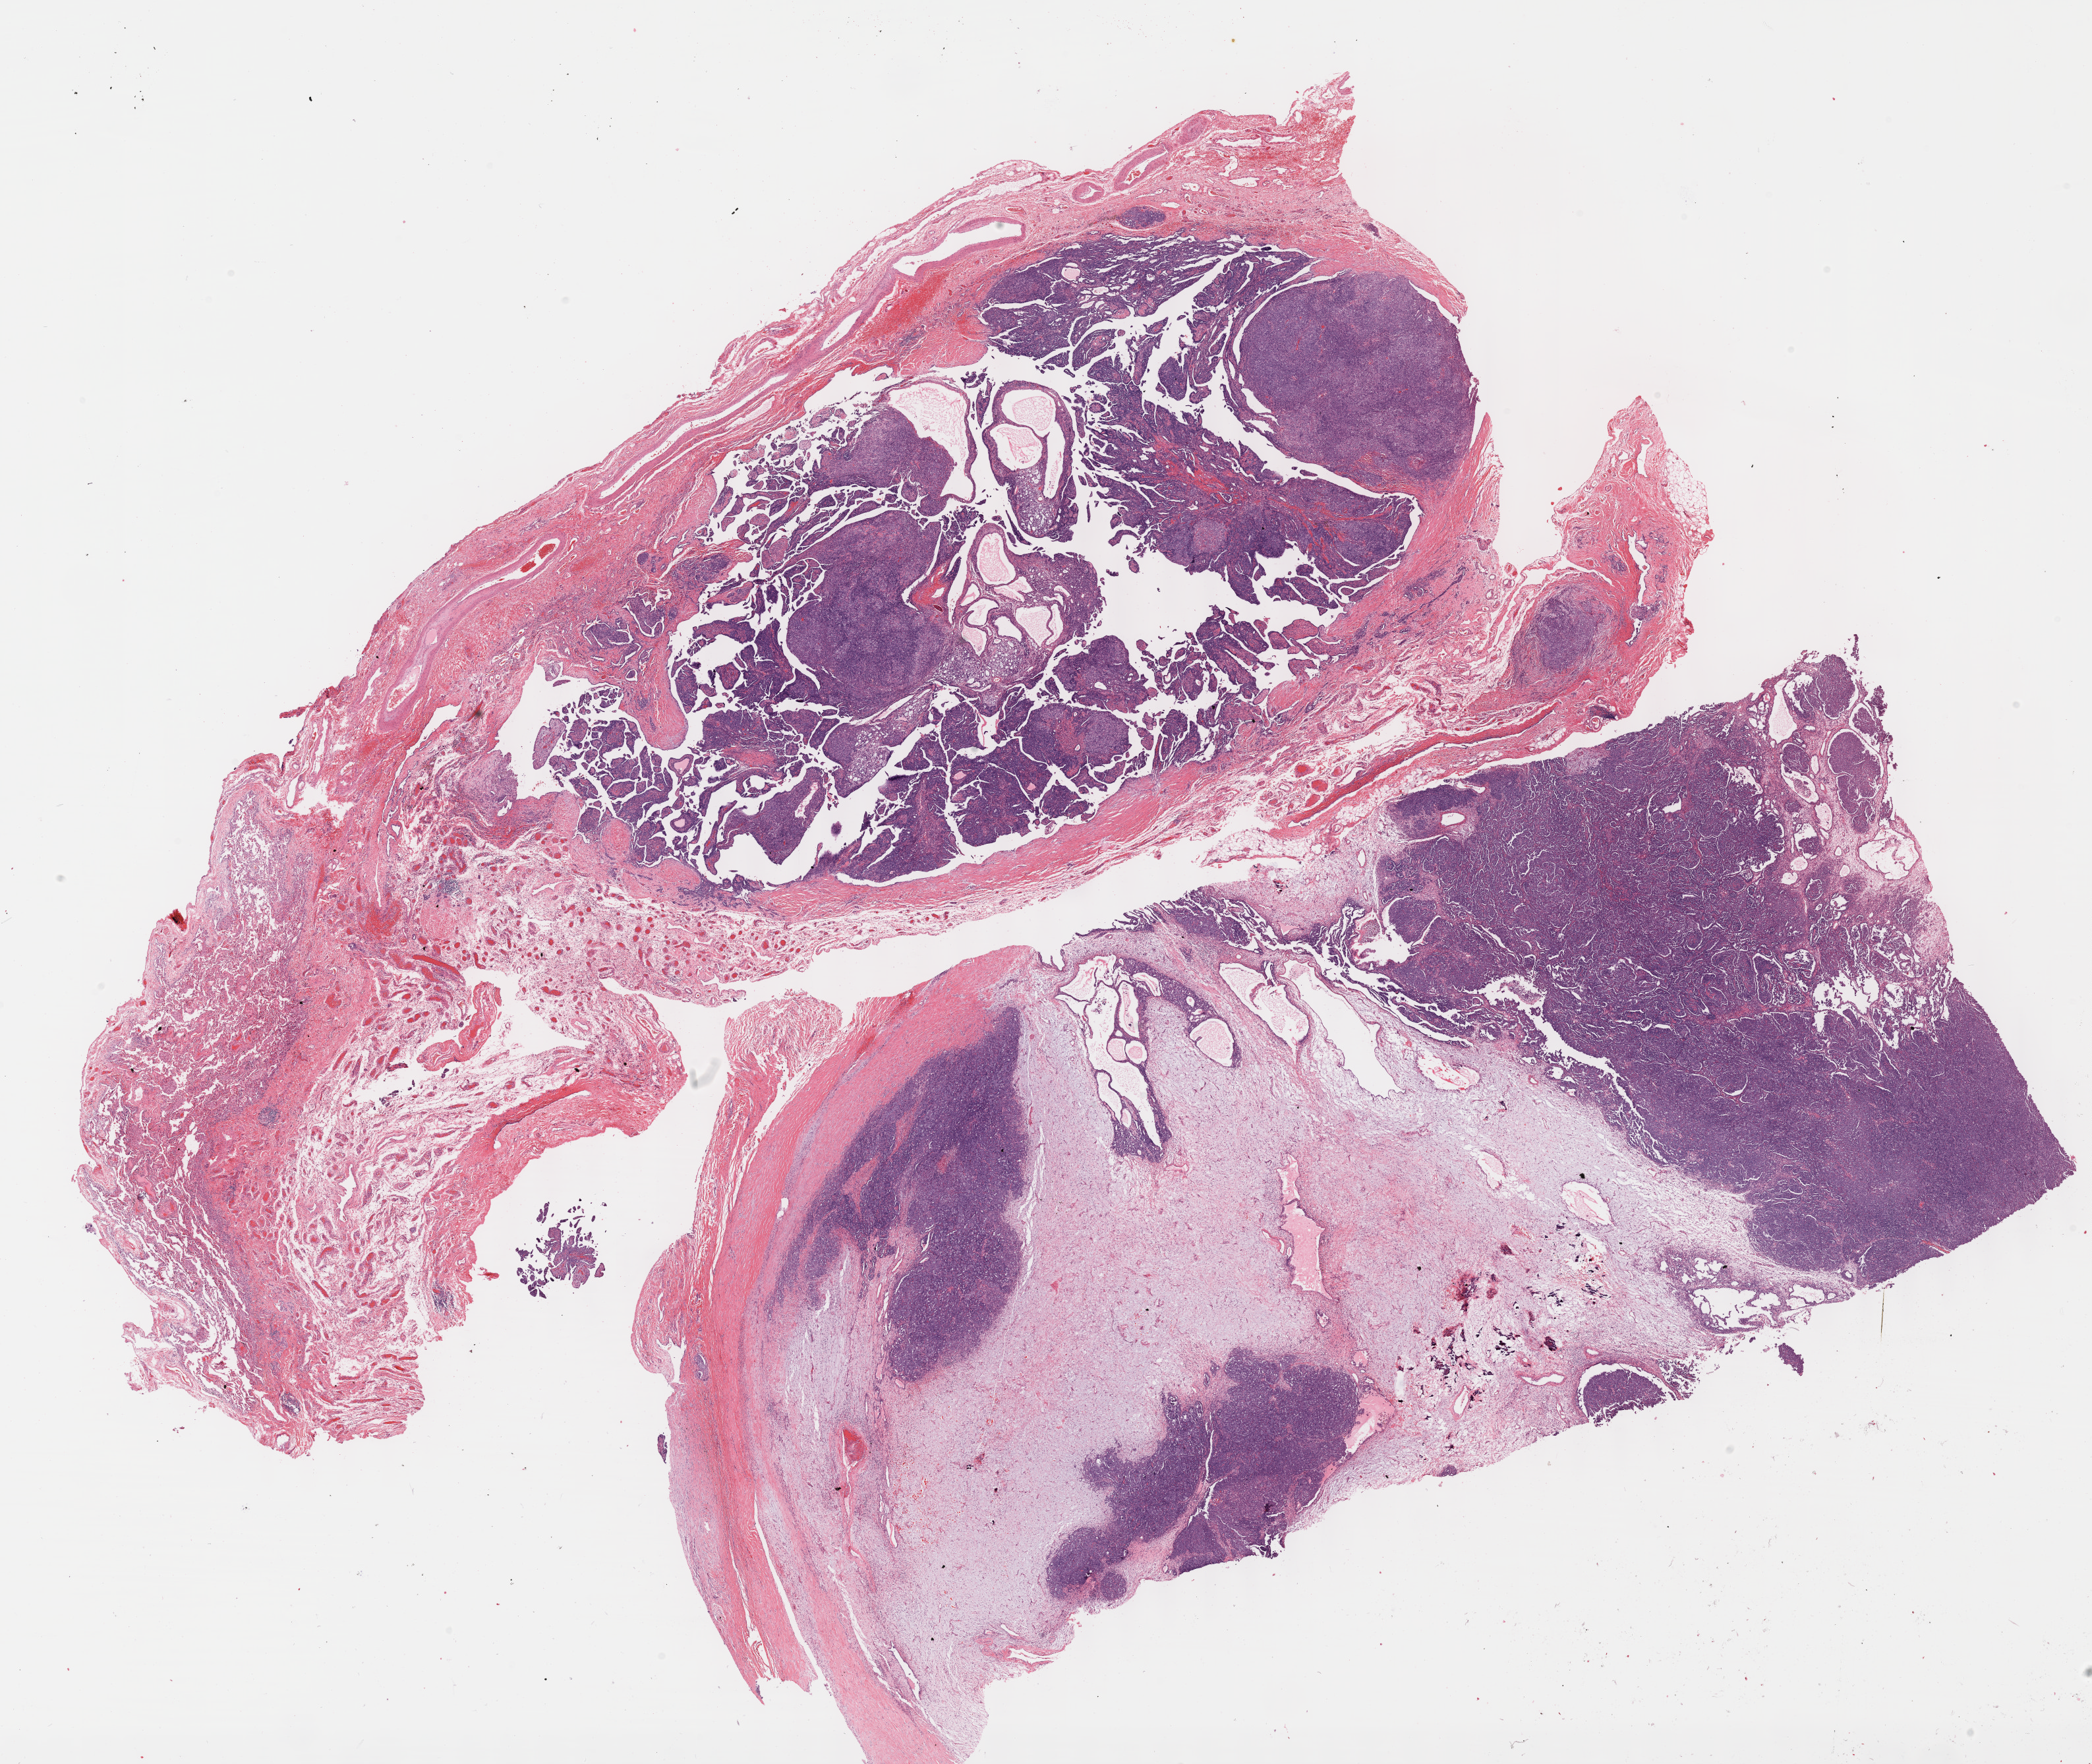
Whole-slide histology image, H&E-stained, a low-resolution overview of the entire scanned area, about 25.7 x 21.6 mm (acquisition: 40x scan), formalin-fixed paraffin-embedded (FFPE) diagnostic section, sample: primary tumour, mesothelium. Patient: male, age at initial diagnosis 68 years.
• diagnosis: Mesothelioma, biphasic, malignant
• AJCC pathologic stage: III (7th edition)